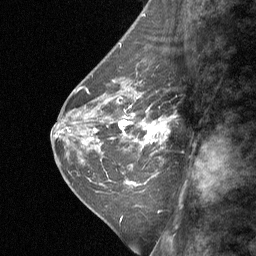
Breast MRI (dynamic contrast-enhanced), one sagittal slice; position 24 of 64 along the scan axis; dynamic contrast-enhanced study with each time point stored as its own series, time point 2 of 3 at this slice position (early post-contrast, ordered by acquisition time); 1.5 T; TE 4.8 ms, TR 27 ms; 2 mm slice thickness; 256 × 256 image matrix, field of view 180 × 180 mm. Female patient, age 42 years. From the clinical record (not read from this slice): setting: breast cancer imaged before/during neoadjuvant chemotherapy; receptor status: triple-negative.
Structures marked on this image (semi-automatic segmentation, software-assisted and operator-edited):
- analysis volume of interest (the breast-tissue region the enhancement analysis was run in; not a lesion): bounding box <124,94,170,161> (left, top, right, bottom; pixels)
- tumour enhancement mask (voxels above the 90 % enhancement threshold inside the analysis volume of interest): <135,121,167,144>